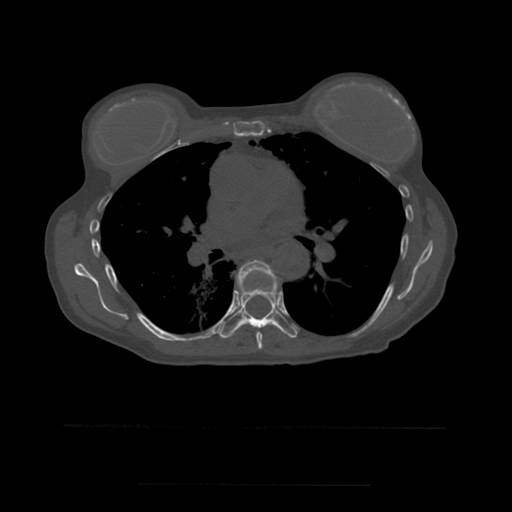
CT including the spine, one axial slice; position 364 of 544 along the scan axis; bone window (W 1800 / L 400 HU); 512 × 512 image matrix, field of view 350 × 350 mm. Patient age 58 years. Case-level facts recorded for this patient, not image findings: primary cancer: lung.
Annotated regions visible in this slice (semi-automatically segmented with operator editing):
- T6 vertebra: bounding box <237,260,281,349> (left, top, right, bottom; pixels)
- T7 vertebra: <213,276,299,339>